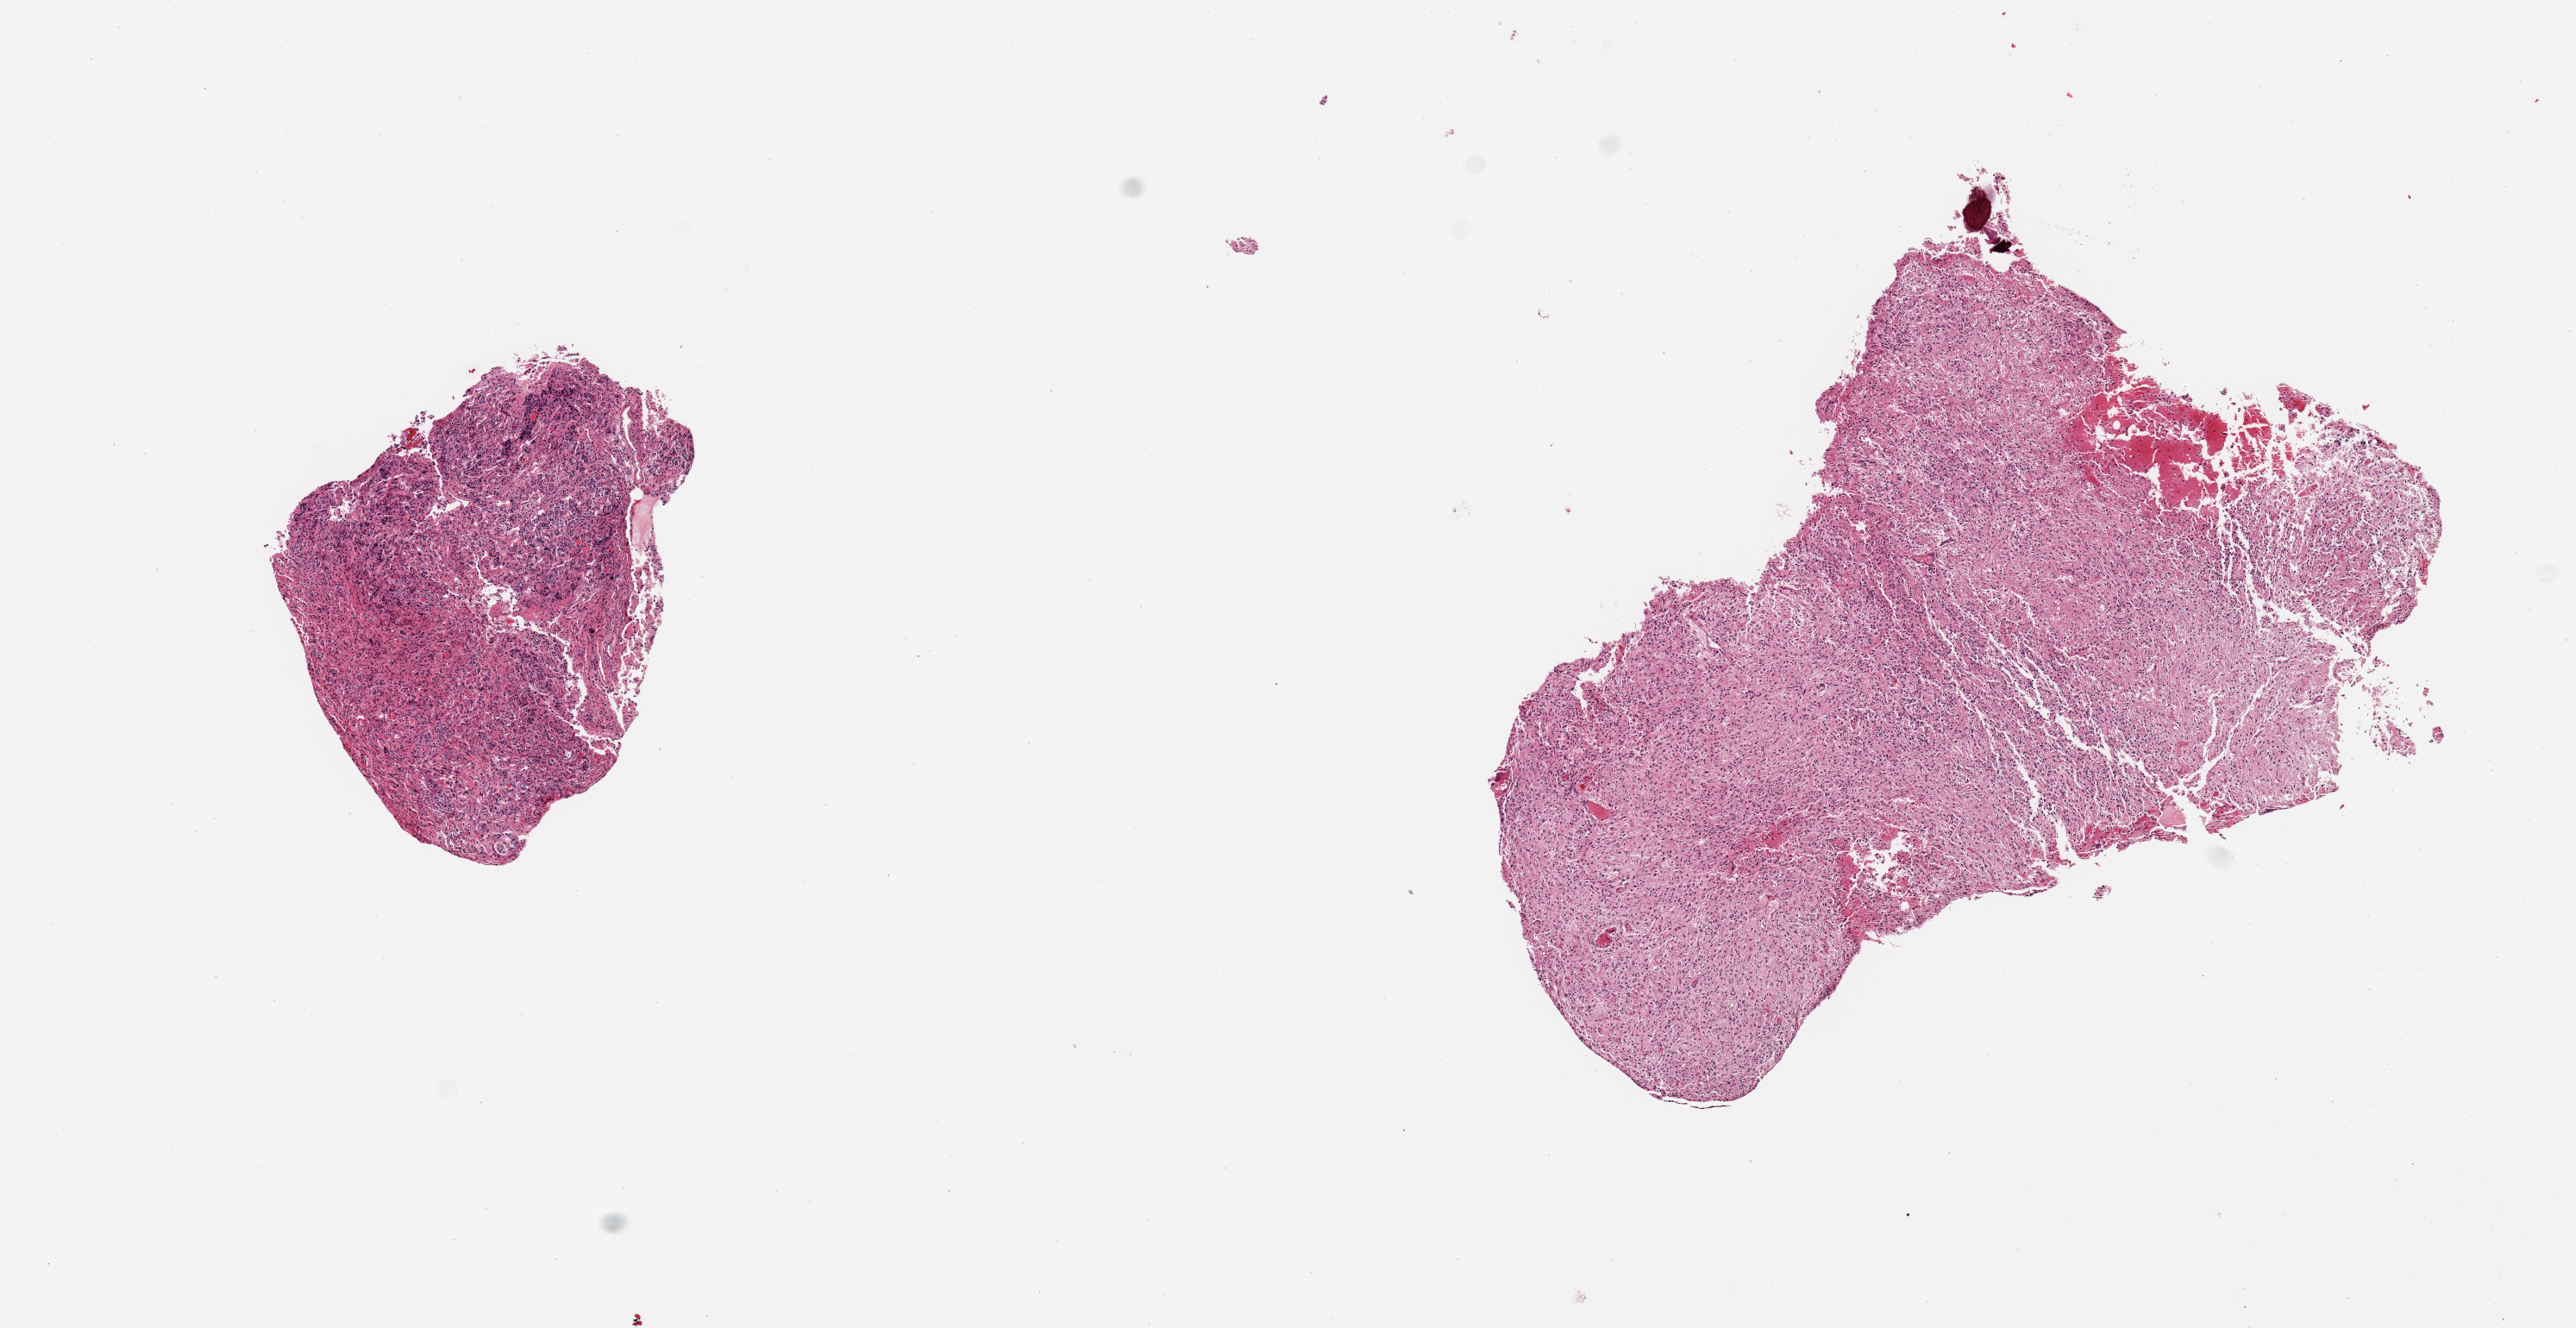
Hematoxylin and eosin (H&E) whole-slide image — shown as a low-resolution overview of the whole scanned area (about 11.8 x 6.1 mm, acquisition: 20x scan); PAXgene-fixed, paraffin-embedded tissue; sampled site (target tissue): pituitary; donor tissue sample. Donor sex: male.
- reviewer comment on this tissue sample: 2 pieces; smaller piece is adenohypophysis (not very robust staining), larger is neurohypophysis